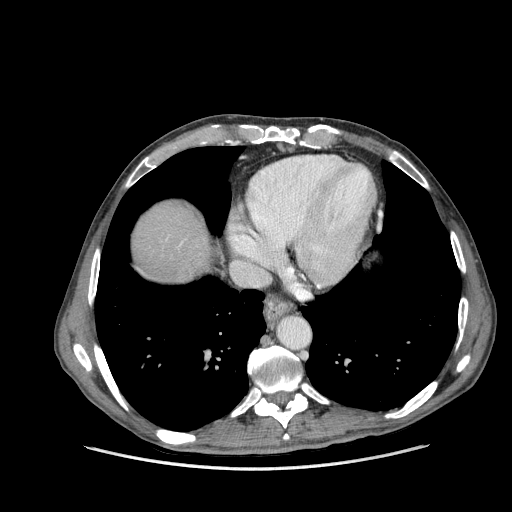
Contrast-enhanced abdominal CT (liver protocol), one axial slice. Slice 141 of 162 in the series (ordered by position). Reconstruction kernel STANDARD. 100 kVp. Soft-tissue window (W 400 / L 40 HU). 2.5 mm slice thickness. 512 × 512 image matrix, field of view 400 × 400 mm. Case-level facts recorded for this patient, not image findings: diagnosis: hepatocellular carcinoma (patient treated with transarterial chemoembolisation; whether this scan precedes or follows treatment is not stated here); TNM stage (as recorded): Stage-IIIA; Child-Pugh class: A; tumour size: 9.9 cm.
Structures marked on this image (semi-automatic segmentation, software-assisted and operator-edited):
- abdominal aorta: bounding box <278,317,309,349> (left, top, right, bottom; pixels)
- liver parenchyma outside the tumour (the mass and vessels are separate outlines, so this box may not span the whole liver): <132,203,209,282>